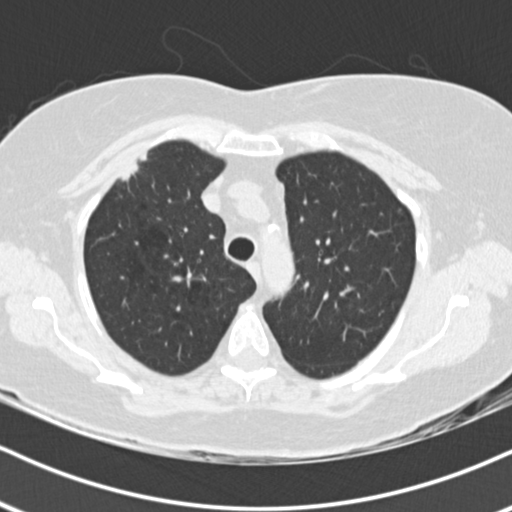
Low-dose screening chest CT, one axial slice. Position 140 of 178 along the scan axis. Reconstruction kernel B30f. Lung window (W 1500 / L -600 HU). 2 mm slice thickness. 512 × 512 image matrix, field of view 320 × 320 mm.
Annotated regions visible in this slice (manually delineated by an expert):
- lesion 1 (tumor, upper lobe of right lung): bounding box [x1, y1, x2, y2] px = [118, 152, 148, 182]